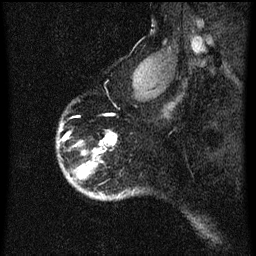
Breast MRI (dynamic contrast-enhanced), one sagittal slice; position 52 of 60 along the scan axis; dynamic contrast-enhanced series, image 2 of 3 at this slice position (ordered by acquisition); 1.5 T; TE 4.2 ms, TR 8 ms; 256 × 256 image matrix, field of view 180 × 180 mm. Female patient, age 56 years.
Structures marked on this image (semi-automatically segmented with operator editing):
- analysis volume of interest (the breast-tissue region the enhancement analysis was run in; not a lesion): bounding box (x1, y1, x2, y2) in pixels: (58, 132, 125, 201)
- tumour enhancement mask (voxels above the 70 % enhancement threshold inside the analysis volume of interest): (74, 134, 117, 179)